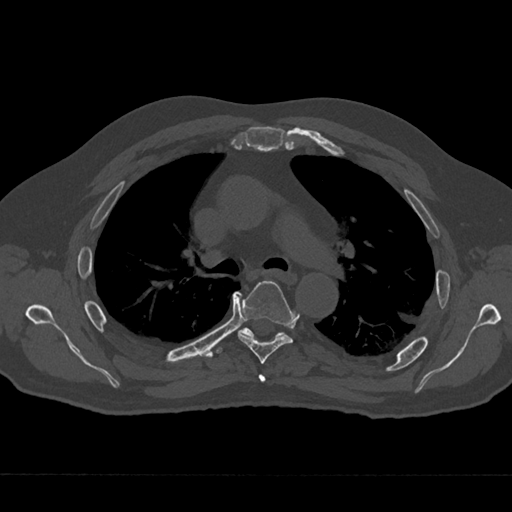
CT including the spine, one axial slice; slice 462 of 797 in the series (ordered by position); 120 kVp; bone window (W 1800 / L 400 HU); 0.5 mm slice thickness; 512 × 512 image matrix. Male patient, age 75 years. From the clinical record (not read from this slice): primary cancer: renal; vertebrae with lytic lesions (as recorded): T4.
Annotated regions visible in this slice (semi-automatically segmented with operator editing):
- T4 vertebra: bounding box <258,374,265,382> (left, top, right, bottom; pixels)
- T5 vertebra: <238,281,294,364>
- T6 vertebra: <239,328,284,338>